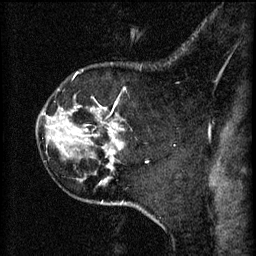
Breast MRI (dynamic contrast-enhanced), one sagittal slice; position 50 of 60 along the scan axis; 3 images stored at this slice position (order not interpretable as contrast timing); 1.5 T; TE 4.2 ms, TR 11 ms; 2 mm slice thickness; 256 × 256 image matrix, field of view 180 × 180 mm. Patient: female, 45 years.
Outlined on this slice (semi-automatic segmentation, software-assisted and operator-edited):
- analysis volume of interest (the breast-tissue region the enhancement analysis was run in; not a lesion): bounding box (x1, y1, x2, y2) in pixels: (104, 128, 127, 171)
- tumour enhancement mask (voxels above the 70 % enhancement threshold inside the analysis volume of interest): (110, 140, 119, 151)